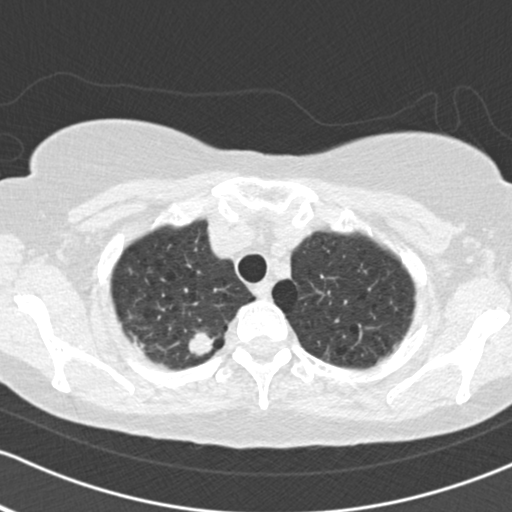
Low-dose screening chest CT, one axial slice. Slice 142 of 161 in the series (ordered by position). Reconstruction kernel B30f. 120 kVp. Lung window (W 1500 / L -600 HU). 512 × 512 image matrix, field of view 312 × 312 mm.
Structures marked on this image (manually delineated by an expert):
- lesion 1 (tumor, upper lobe of right lung): bounding box (x1, y1, x2, y2) in pixels: (189, 330, 215, 356)